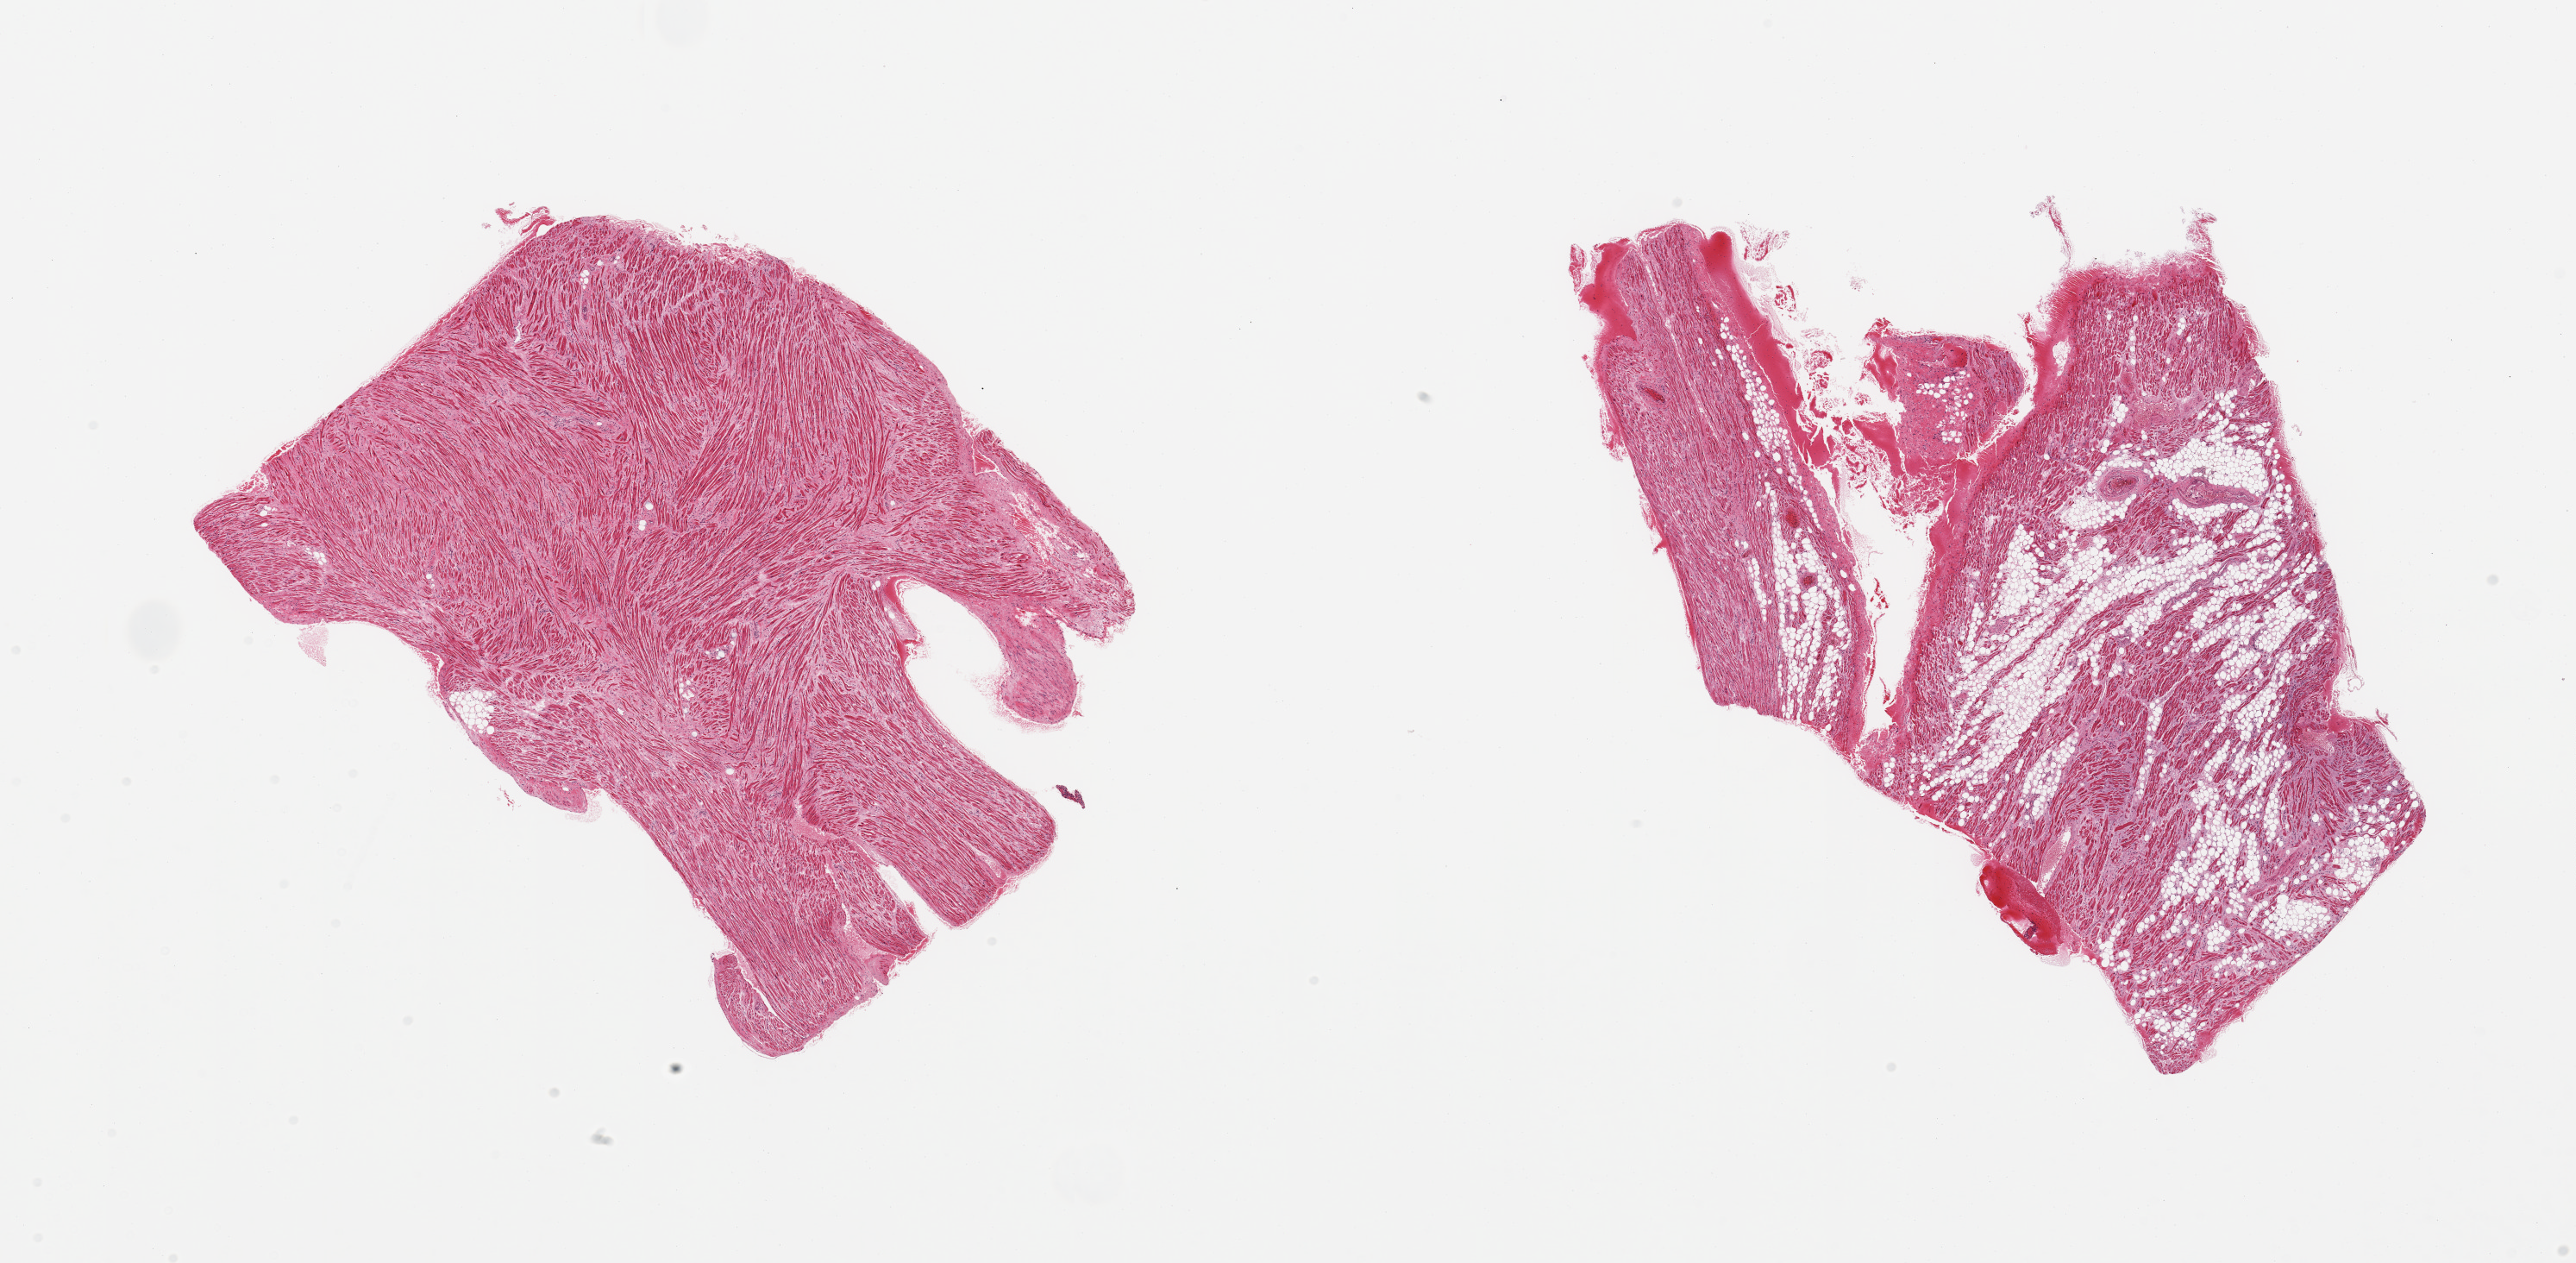
Digitized haematoxylin and eosin-stained section — whole scanned area (about 23.6 x 11.6 mm) shown as a low-resolution overview. PAXgene-fixed, paraffin-embedded tissue. Sampled site (target tissue): auricular appendage. Donor tissue sample. Female donor.
- review note (as recorded): 2 pieces; 1 all muscle. other 50% fat